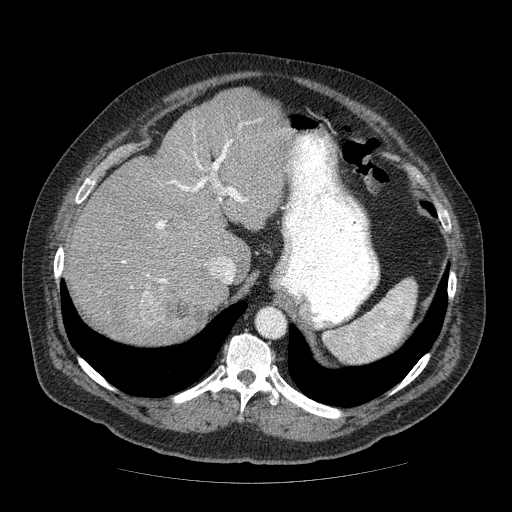
Contrast-enhanced abdominal CT (liver protocol), one axial slice. Position 47 of 85 along the scan axis. 120 kVp. Soft-tissue window (W 400 / L 40 HU). 2.5 mm slice thickness. 512 × 512 image matrix, field of view 420 × 420 mm. Case-level facts recorded for this patient, not image findings: diagnosis: hepatocellular carcinoma (patient treated with transarterial chemoembolisation; whether this scan precedes or follows treatment is not stated here); TNM stage (as recorded): Stage-IIIA; Child-Pugh class: A; tumour nodularity: multinodular; tumour size: 7 cm.
Annotated regions visible in this slice (semi-automatically segmented with operator editing):
- abdominal aorta: box from (x=256, y=307) to (x=284, y=337) px
- liver parenchyma outside the tumour (the mass and vessels are separate outlines, so this box may not span the whole liver): (x=66, y=88)–(x=294, y=344)
- mass: (x=138, y=284)–(x=204, y=342)
- liver vessels: (x=122, y=124)–(x=247, y=289)